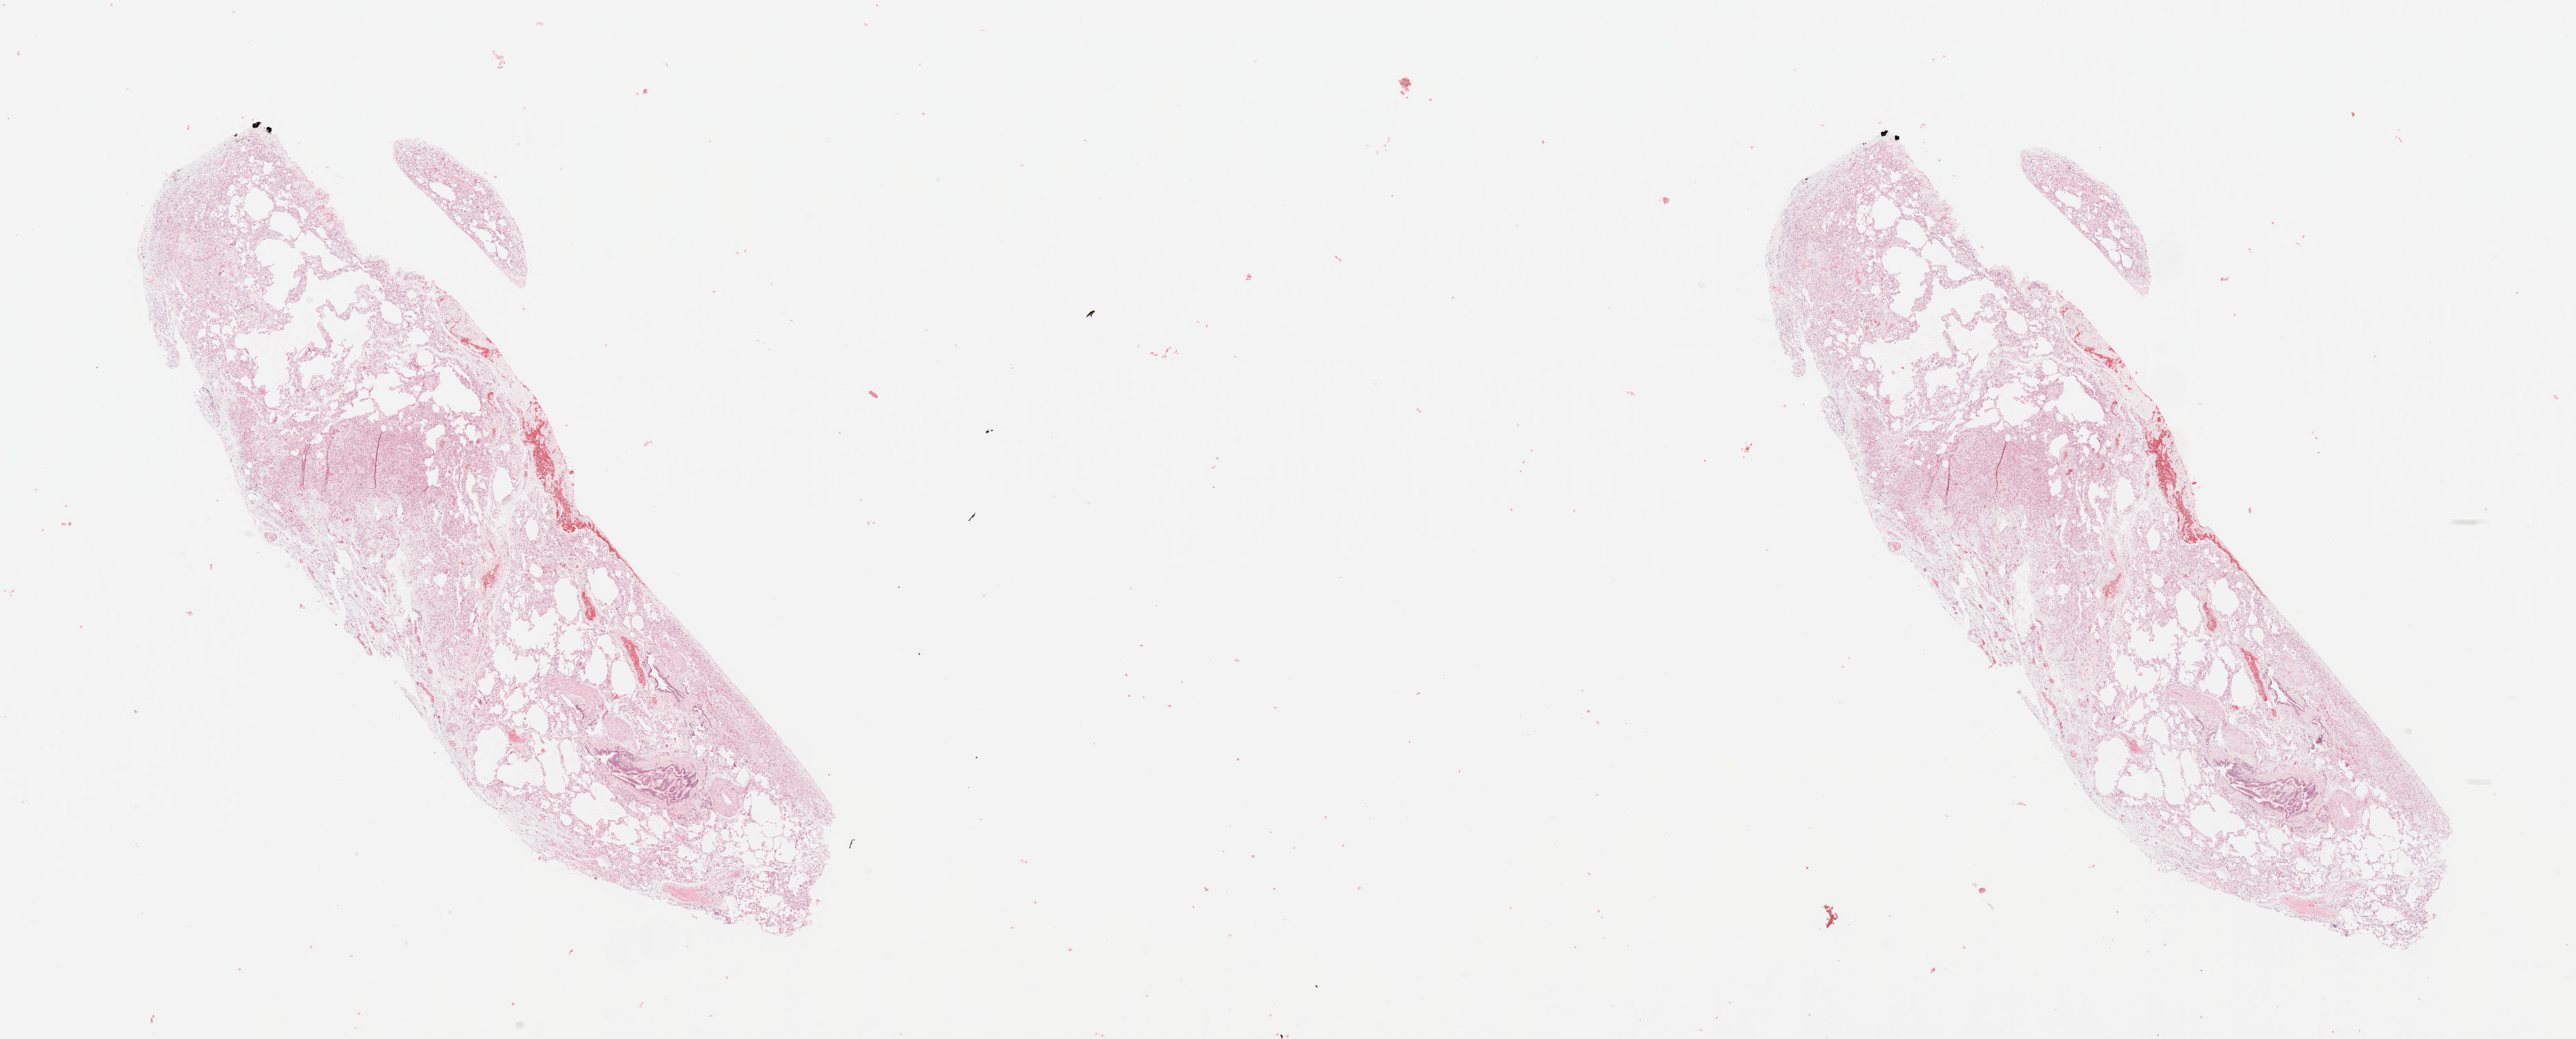
Whole-slide histology image, H&E — whole scanned area (about 29.5 x 11.9 mm) shown as a low-resolution overview, lung, normal (non-tumour) tissue. Patient: female, age 66 years.
This section: normal (non-tumour) tissue from the same patient. Patient diagnosis: Squamous cell carcinoma, NOS.